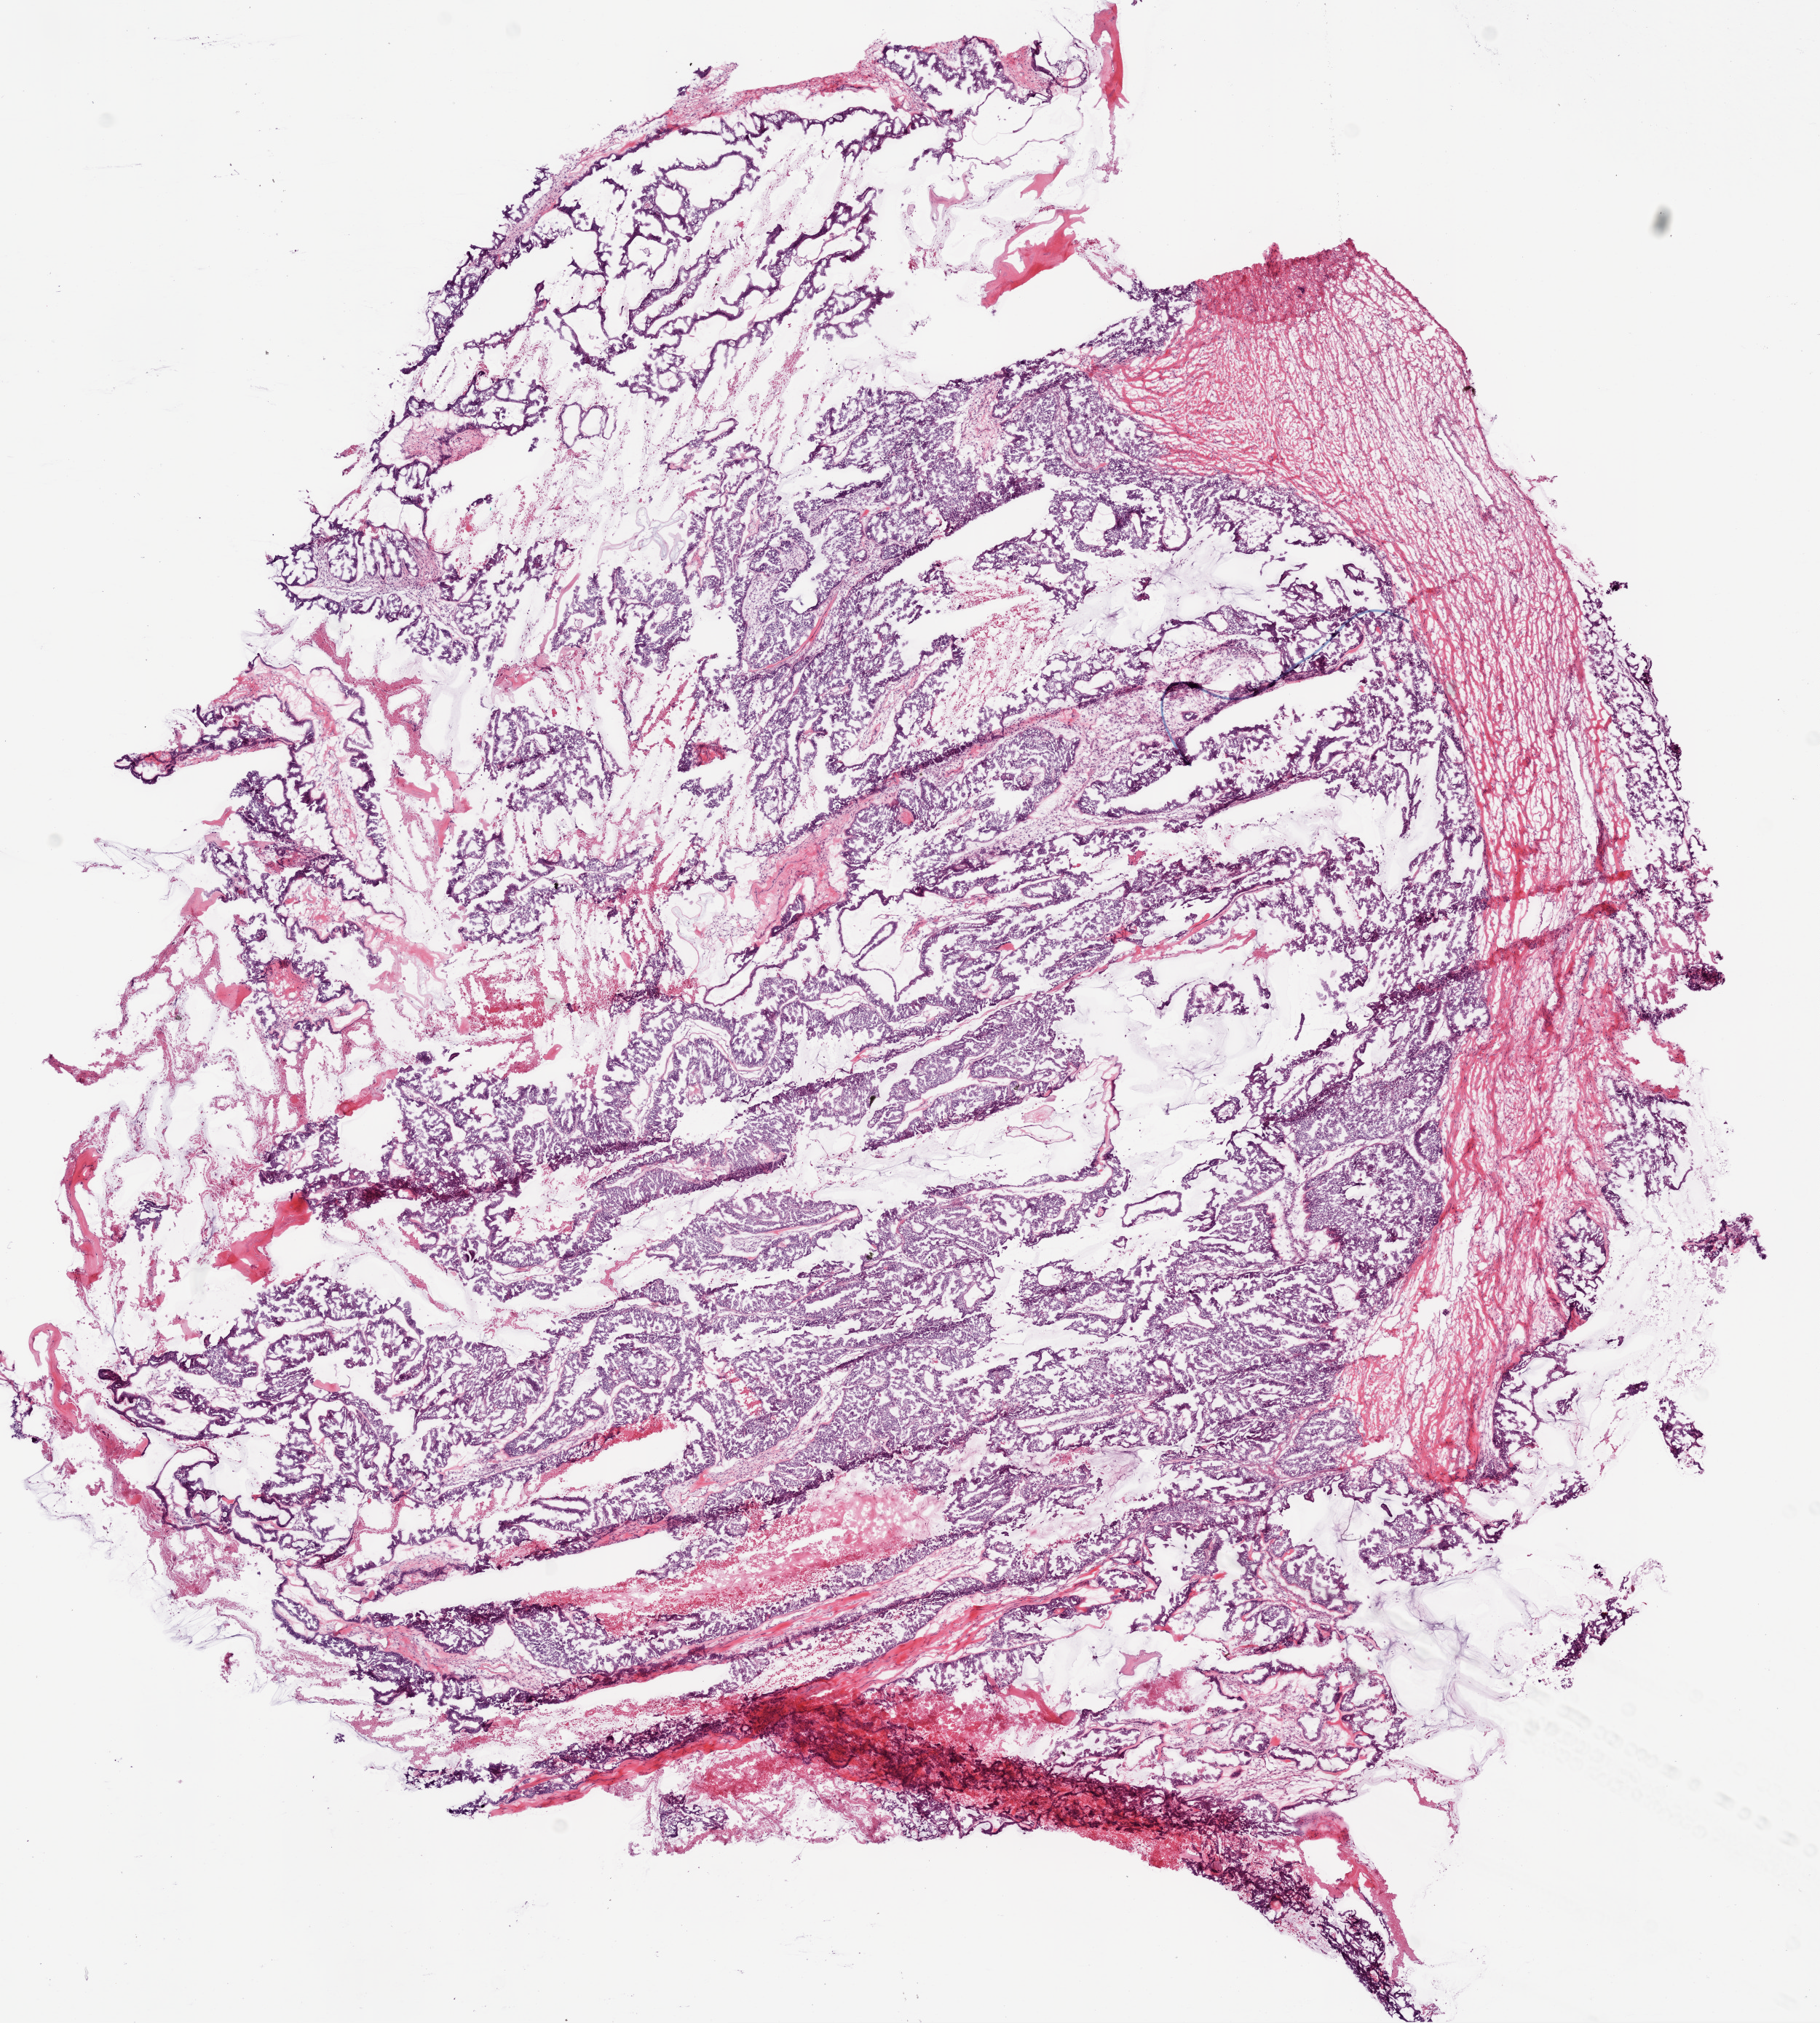
Hematoxylin and eosin (H&E) stained whole-slide image — shown as a low-resolution overview of the whole scanned area (about 10.0 x 11.1 mm, acquisition: 20x scan). Frozen section. Ovary, primary tumour sample. Patient: female, age at initial diagnosis 71 years. Histologic grade: G3 (poorly differentiated). Composition of this section per pathologist review: tumour cells 70%, tumour nuclei 80%, normal cells 0%, stromal cells 20%, necrosis 10%.
- histologic diagnosis: Serous cystadenocarcinoma, NOS
- FIGO stage: IIIC